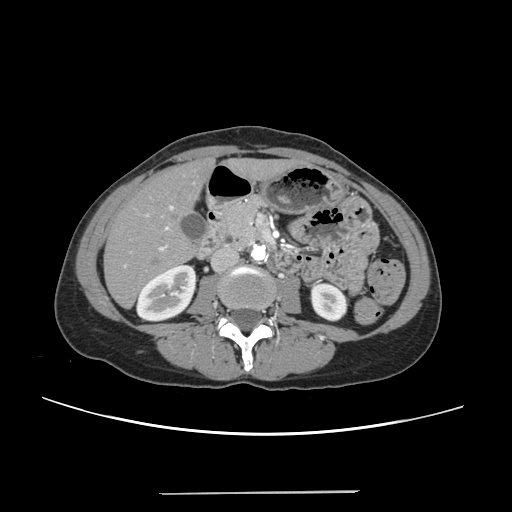
Contrast-enhanced abdominal CT, one axial slice. Slice 90 of 240 in the series (ordered by position). Intravenous contrast given. Soft-tissue window (W 400 / L 40 HU). 1.25 mm slice thickness. 512 × 512 image matrix, field of view 371 × 371 mm. Female patient, age 60 years. From the clinical record (not read from this slice): diagnosis: colorectal cancer liver metastases, imaged before liver resection; multiple liver metastases: no; largest metastasis: 1.5 cm; disease in both lobes: no.
Structures marked on this image (expert manual segmentation):
- liver: bounding box (x1, y1, x2, y2) in pixels: (105, 161, 287, 306)
- planned liver remnant (the part of the liver to remain after resection): (105, 162, 287, 306)
- portal vein (with intrahepatic branches): (123, 206, 173, 267)